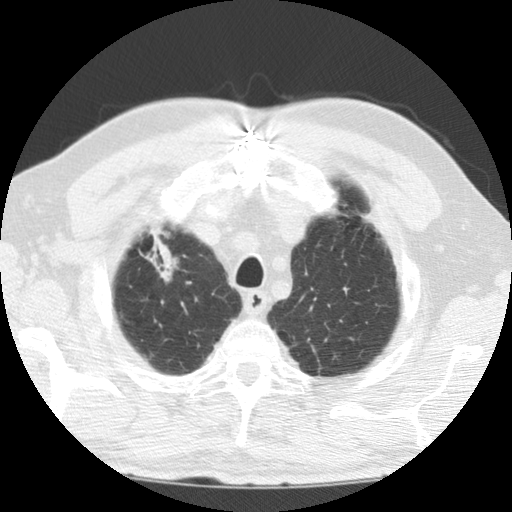
Axial slice from a low-dose chest CT screening exam. First (baseline) screen. Lung window (W 1500 / L -600 HU). Standard (soft-tissue) reconstruction kernel (STANDARD). 120 kVp. 512 × 512 image matrix, field of view 320 × 320 mm. Male, age 69 years at enrolment. Former smoker at enrolment.
- Expert reader's lesion annotation, bounding box <106,216,186,295> (left, top, right, bottom; pixels).
- No non-calcified nodule or mass ≥4 mm was recorded by the screening reader at this exam.
- Official screen result: negative screen, minor abnormalities not suspicious for lung cancer.
- Participant outcome: lung cancer diagnosed 171 days after this screen — adenocarcinoma, NOS, right upper lobe, poorly differentiated (G3), stage IIIB (AJCC 6th edition), 40 mm at pathology.